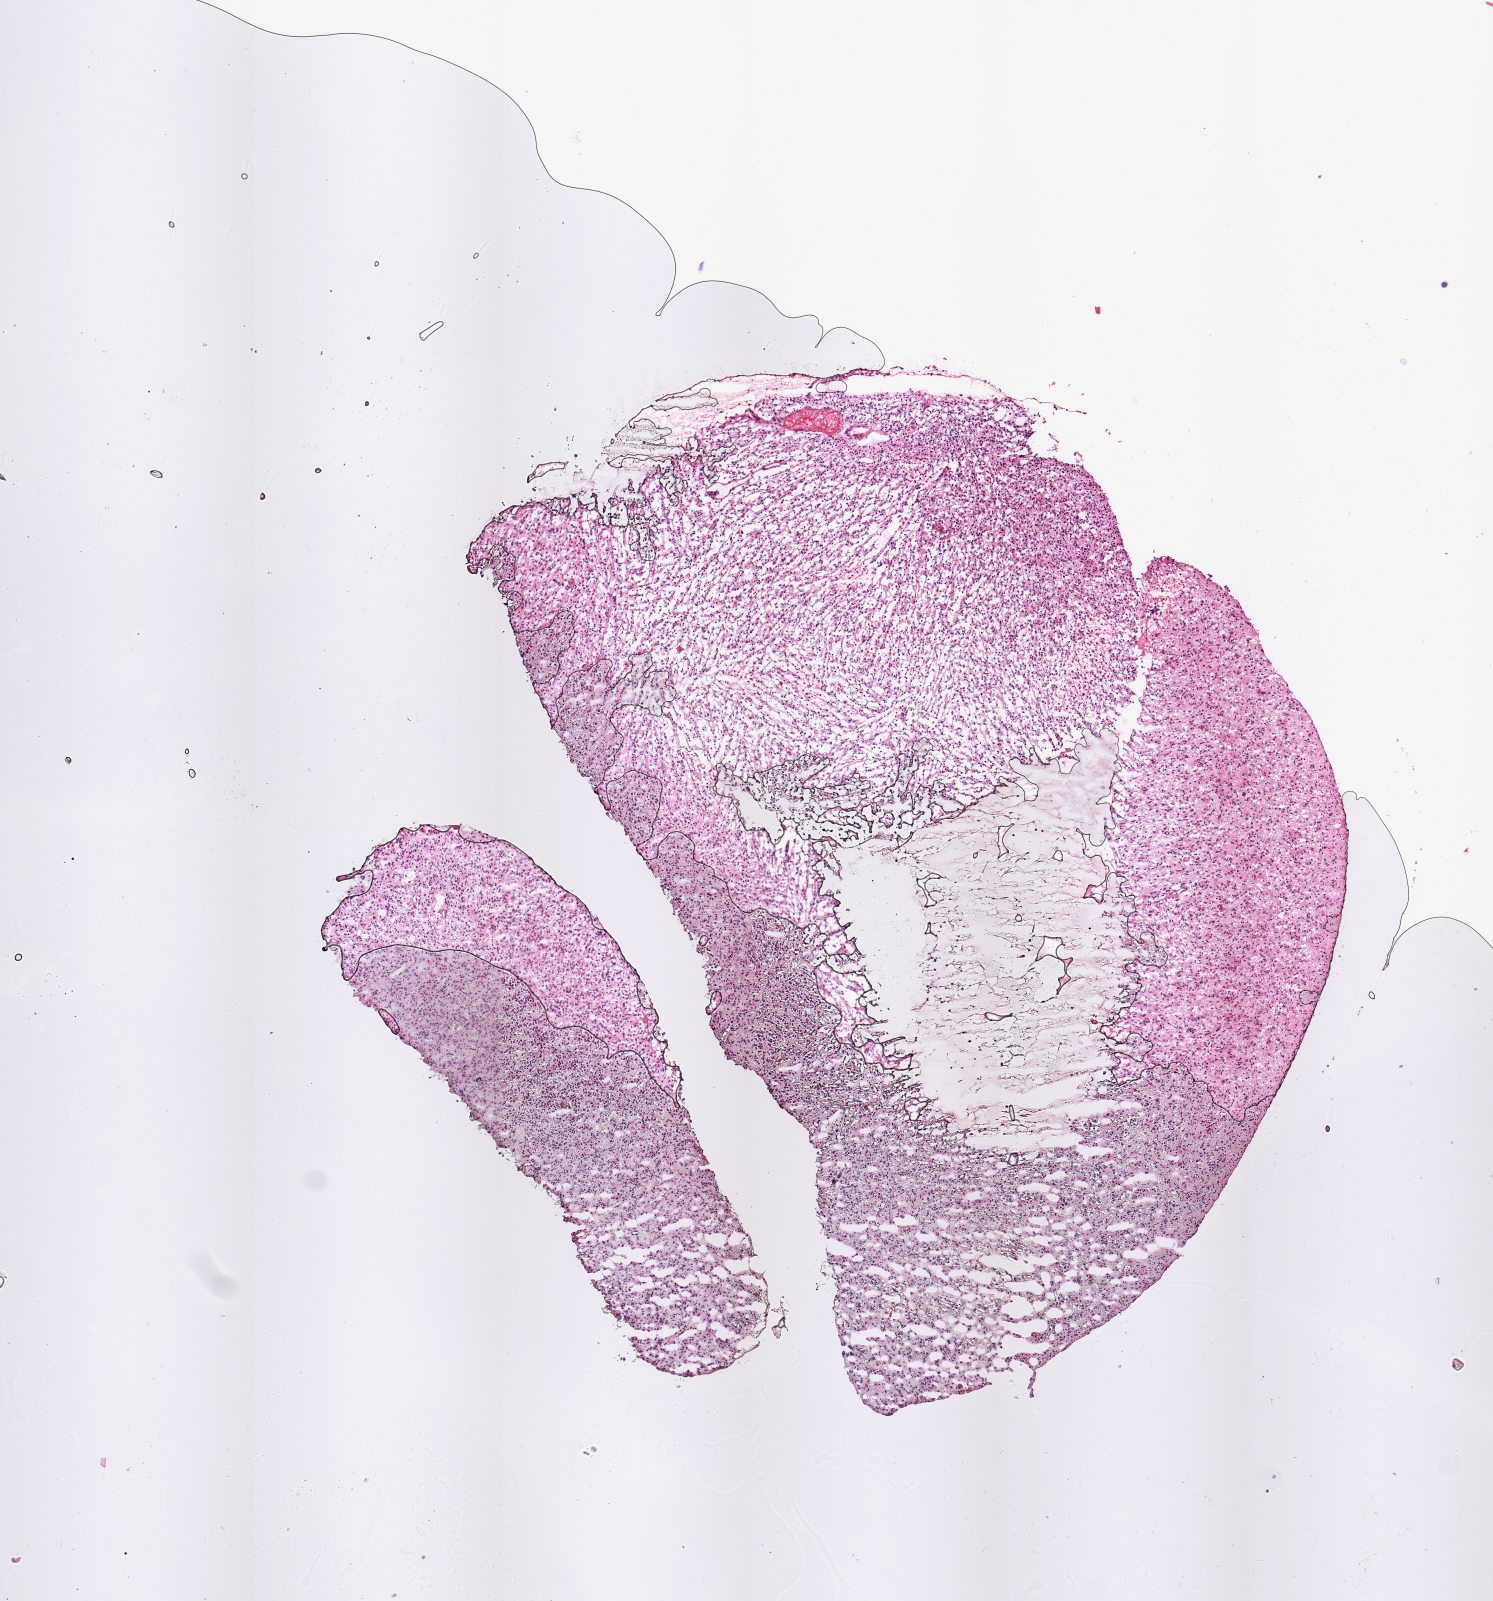
Digitized H&E tissue section (whole slide) — a low-resolution overview of the entire scanned area, about 5.9 x 6.3 mm (from a 20x scan), tumour tissue sample, brain. Patient: female, age 49 years.
Primary tumour site (as recorded): parietal lobe. Patient diagnosis (cohort enrolment): glioblastoma multiforme (brain).